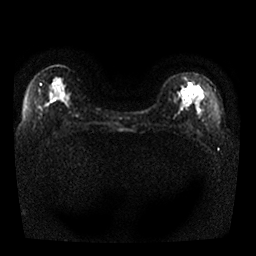
Breast MRI, one axial slice. Slice 14 of 25 in the series (ordered by position). Diffusion-weighted series; image 2 of 4 stored at this slice position (different b-values; order by instance number). 1.5 T. 256 × 256 image matrix, field of view 330 × 330 mm. Female patient.
Structures marked on this image (outlined manually by an expert reader):
- tumour on diffusion-weighted imaging: bounding box (x1, y1, x2, y2) in pixels: (182, 82, 194, 95)